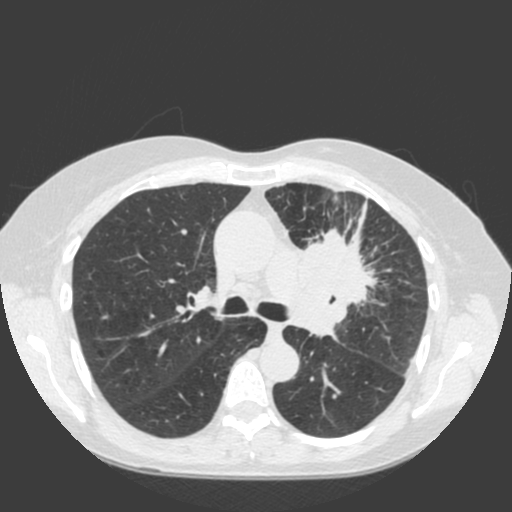
Low-dose screening chest CT, one axial slice. Position 122 of 184 along the scan axis. 120 kVp. Lung window (W 1500 / L -600 HU). 512 × 512 image matrix.
Structures marked on this image (expert manual segmentation):
- lesion 1 (tumor, hilum of left lung): bounding box (x1, y1, x2, y2) in pixels: (290, 231, 378, 335)